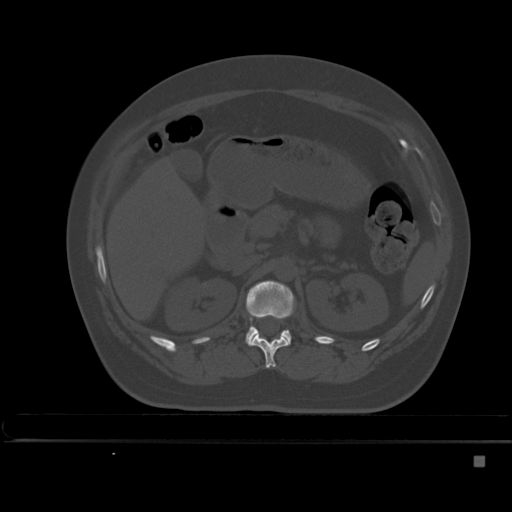
CT including the spine, one axial slice. Position 204 of 495 along the scan axis. Bone window (W 1800 / L 400 HU). 1.5 mm slice thickness. 512 × 512 image matrix, field of view 404 × 404 mm. Female patient, age 33 years. From the clinical record (not read from this slice): primary cancer: breast; vertebrae with lytic lesions (as recorded): T1.
Annotated regions visible in this slice (semi-automatic segmentation, software-assisted and operator-edited):
- L1 vertebra: box from (x=246, y=280) to (x=295, y=345) px
- T12 vertebra: (x=249, y=334)–(x=289, y=368)